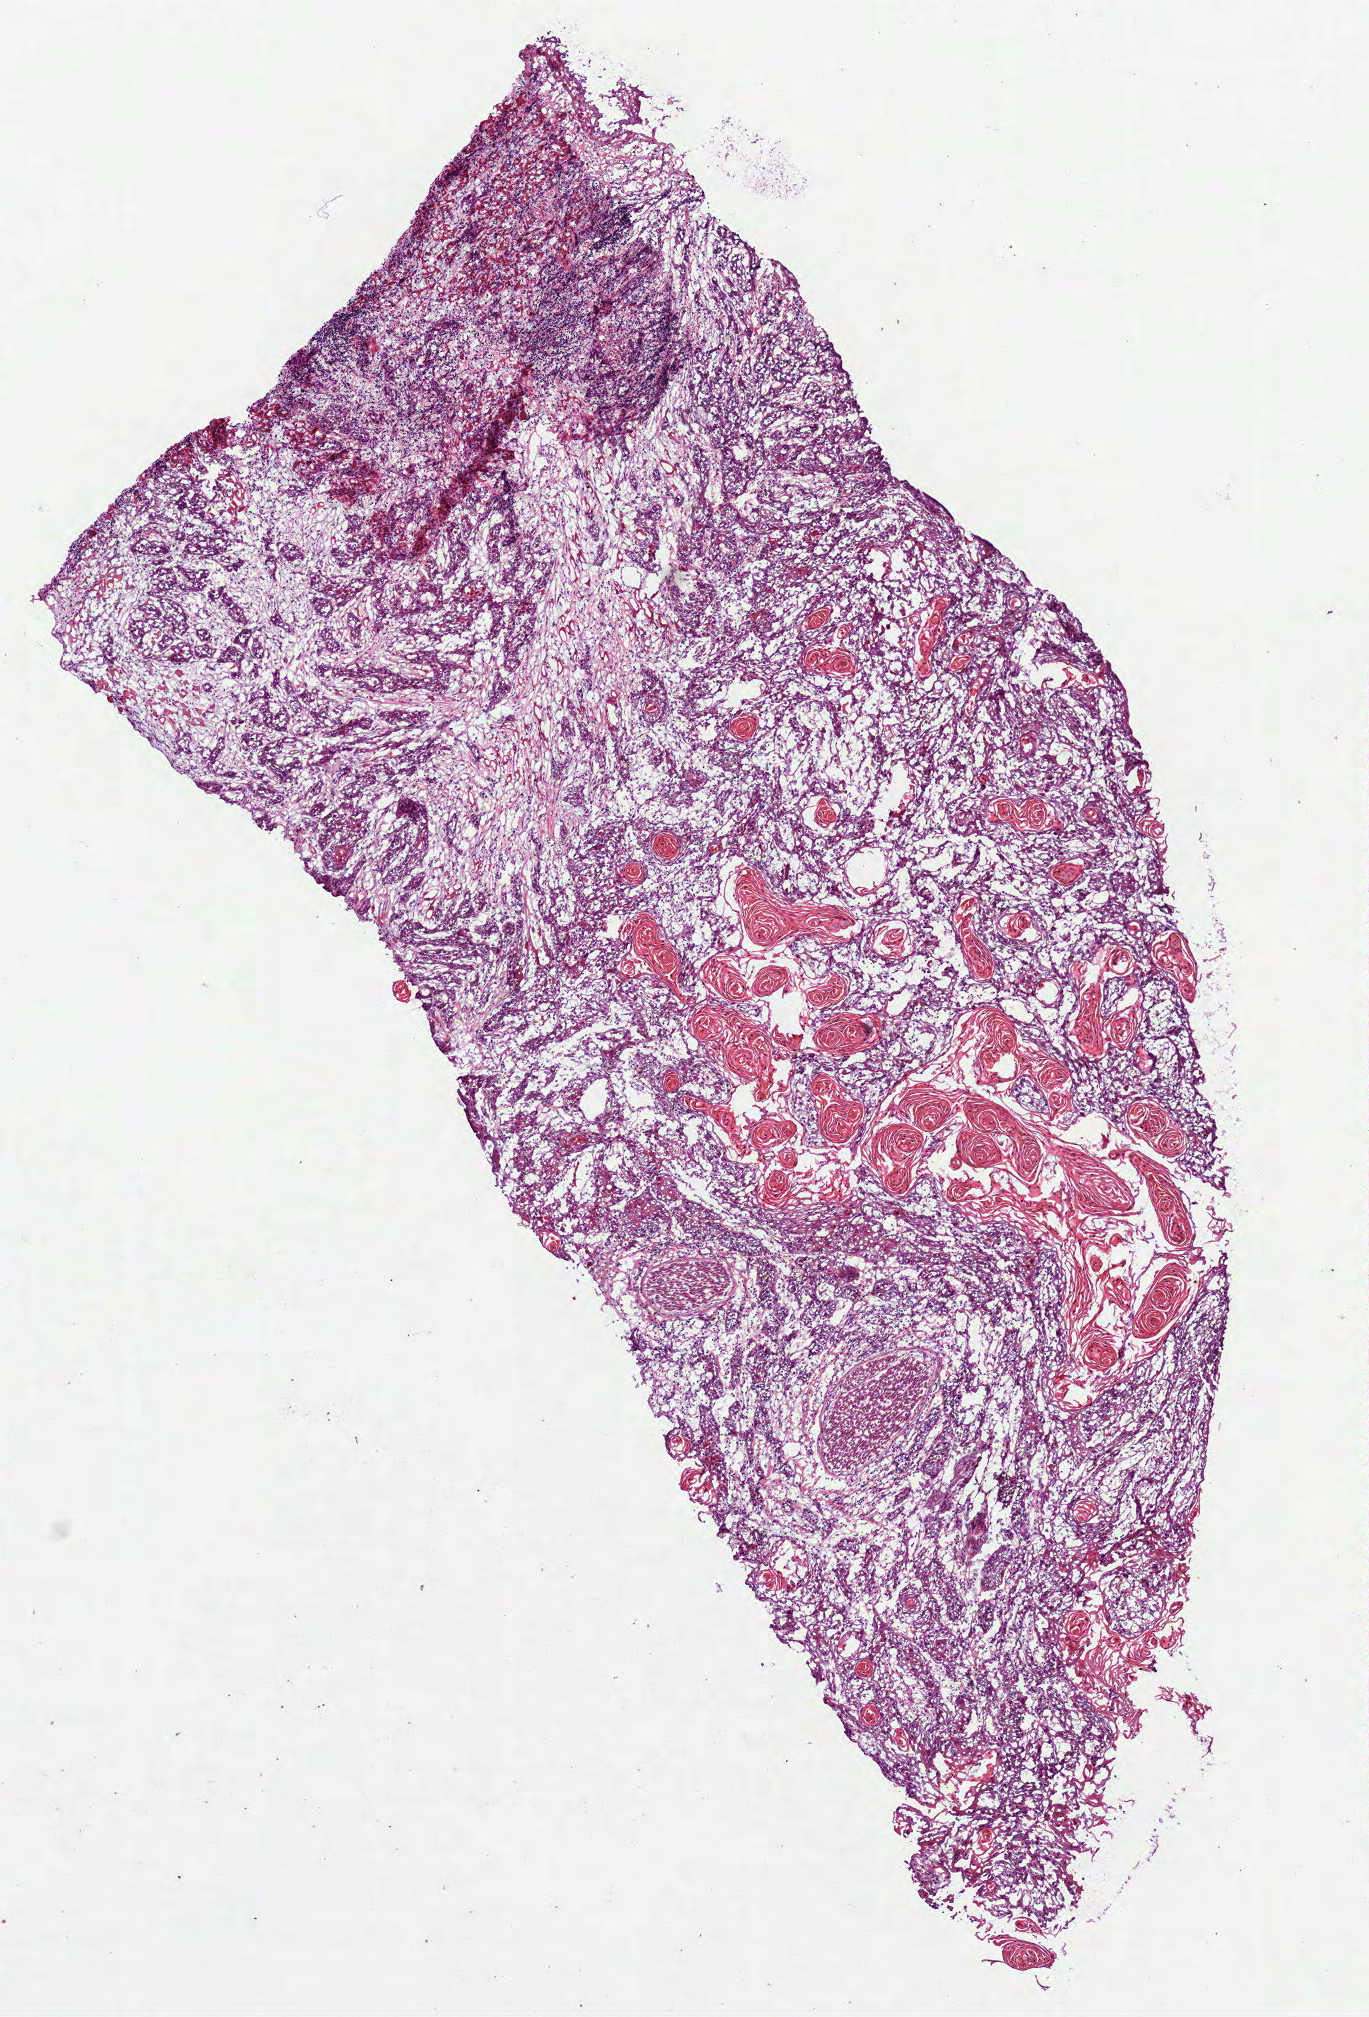
Whole-slide histology image, H&E-stained — shown as a low-resolution overview of the whole scanned area (about 5.5 x 8.1 mm). Frozen section. Sample: primary tumour, head and neck. Male patient; age at initial diagnosis 77 years. Histologic grade: G2 (moderately differentiated). Composition of this section per pathologist review: tumour cells 75%, tumour nuclei 85%, normal cells 0%, stromal cells 25%, necrosis 0%.
• AJCC pathologic stage: IVA
• pathologic diagnosis: Squamous cell carcinoma, NOS
• laterality: left